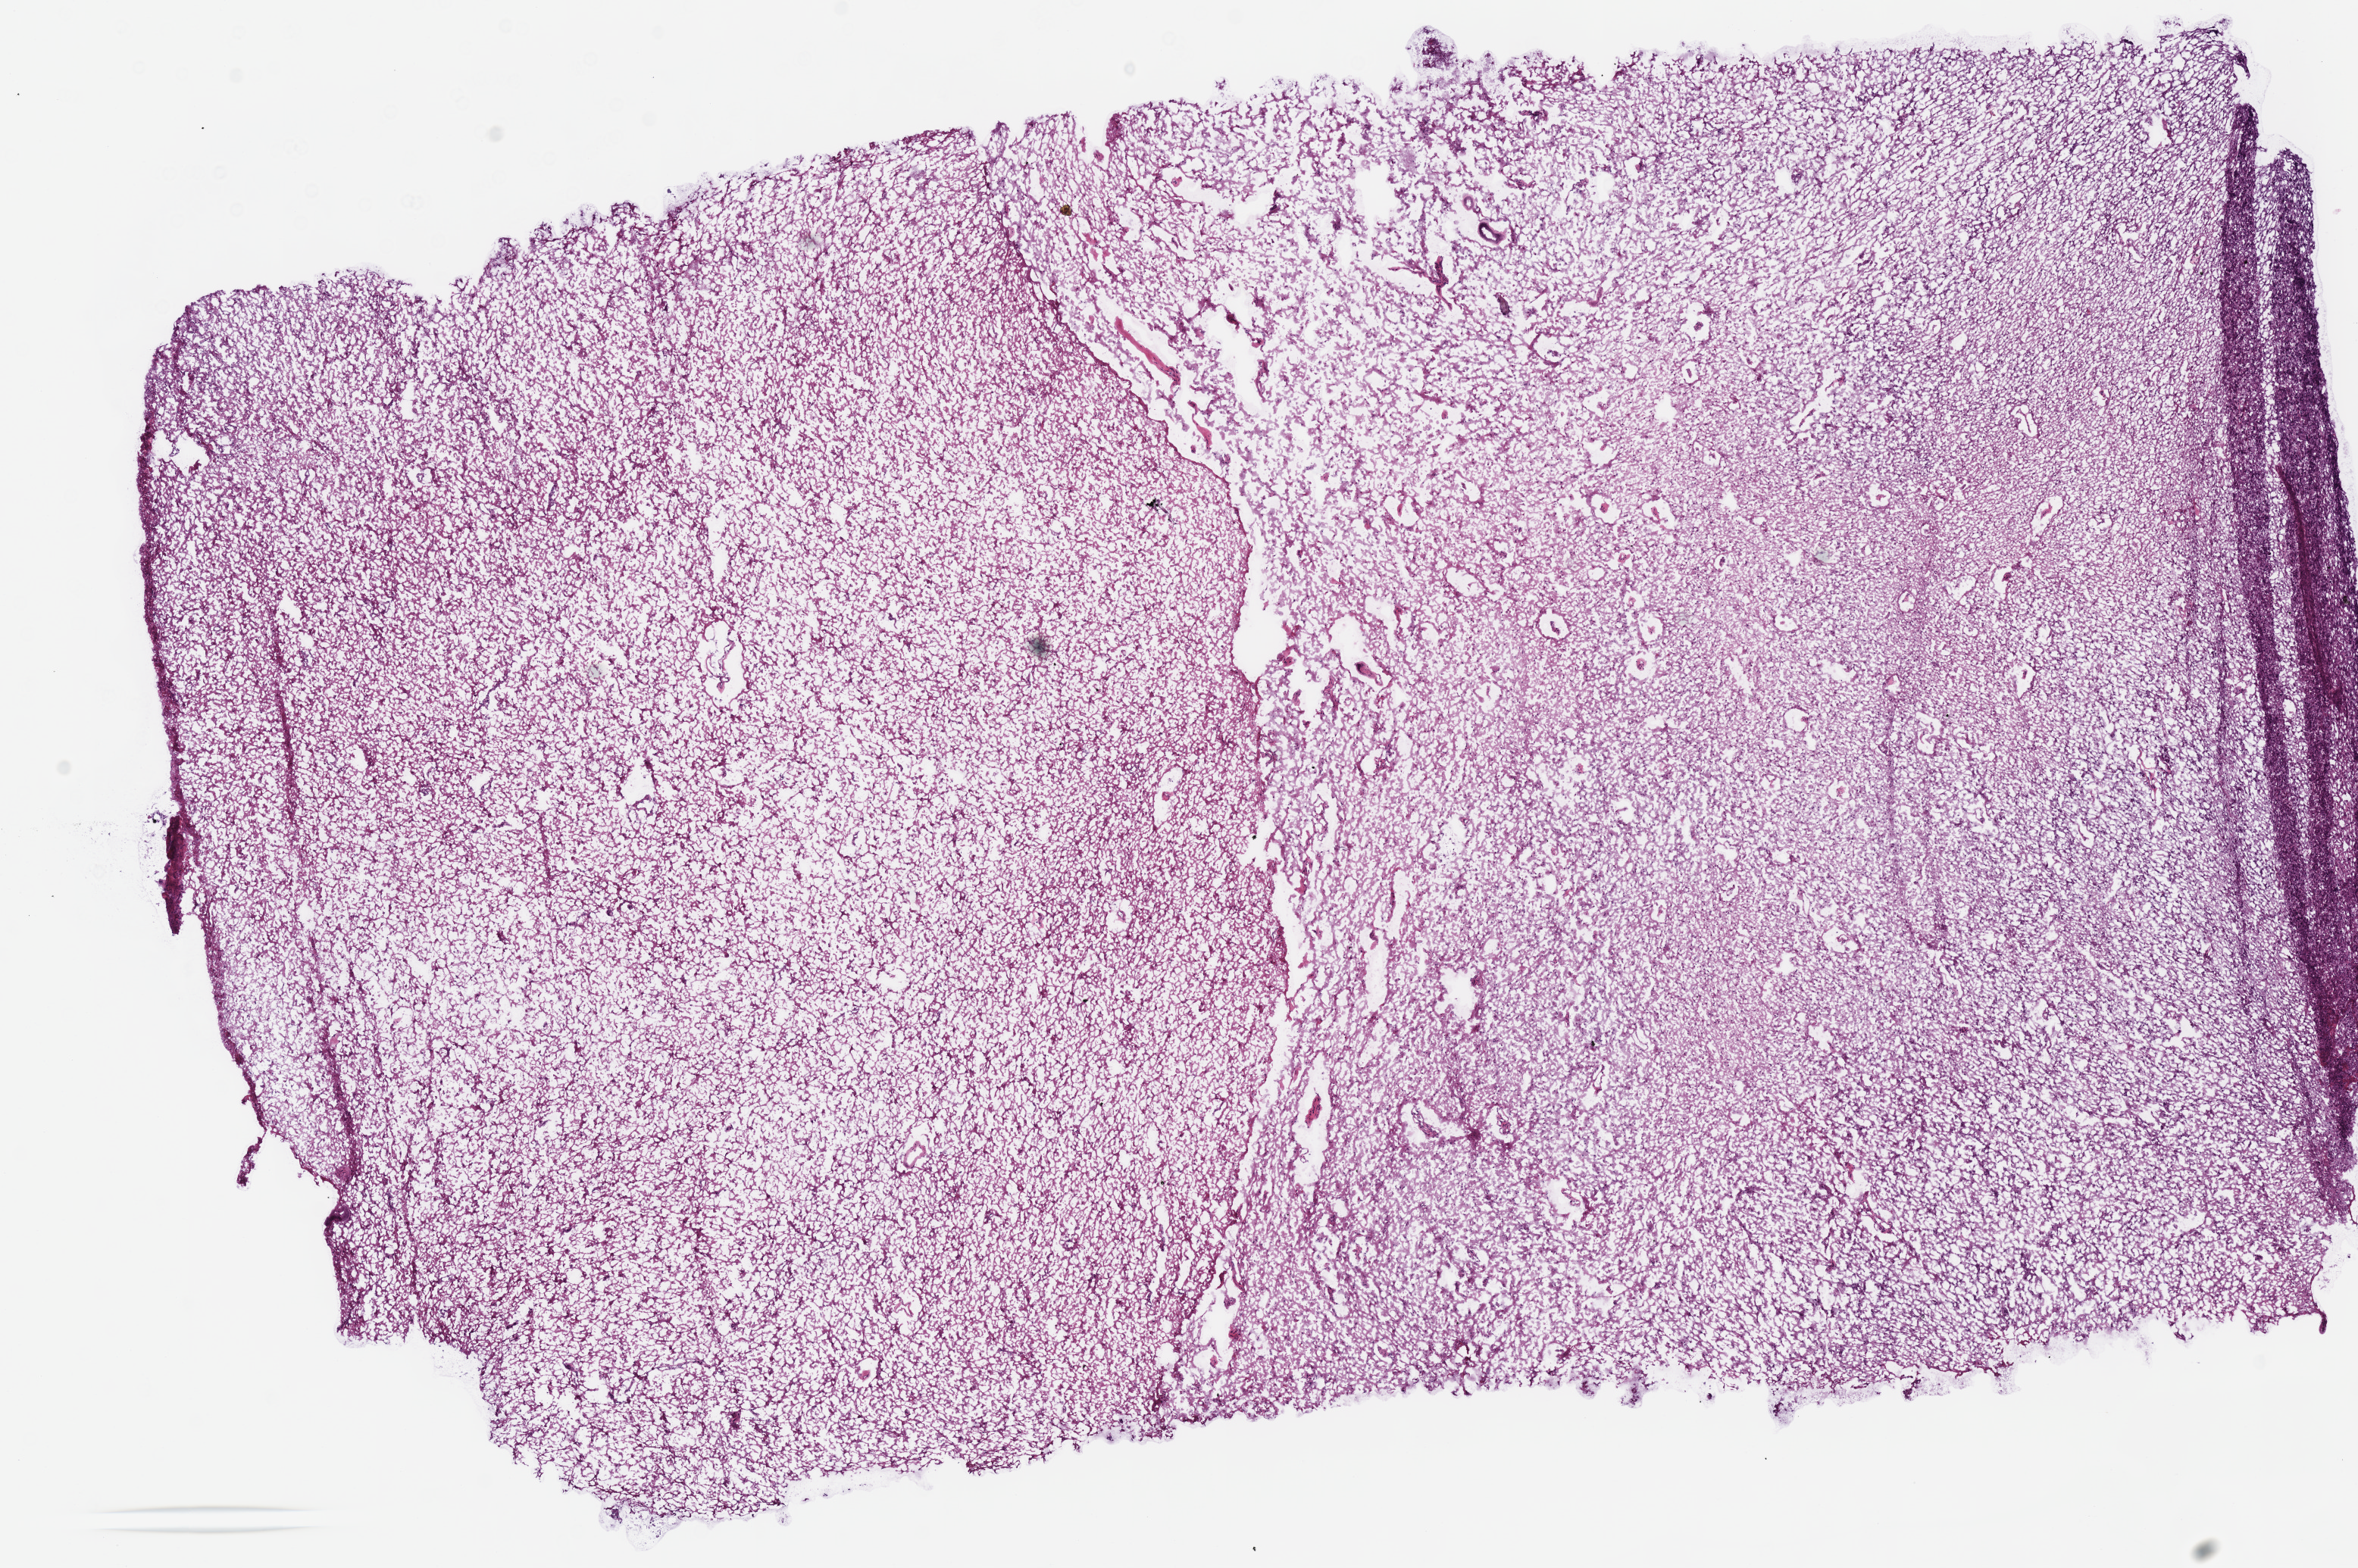
H&E whole-slide image, shown as a low-resolution overview of the whole scanned area (about 12.2 x 8.1 mm, from a 40x scan). Frozen section from the top of the tissue portion. Sample: primary tumour, brain. Male, age 58 years at initial diagnosis.
Diagnosis: Mixed glioma (cerebrum).